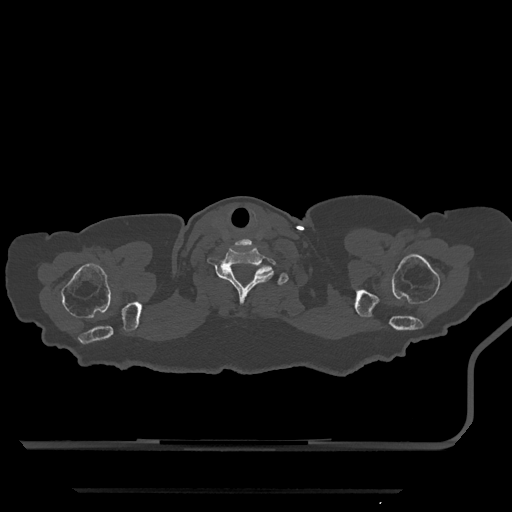
CT including the spine, one axial slice. Slice 735 of 797 in the series (ordered by position). Bone window (W 1800 / L 400 HU). 512 × 512 image matrix, field of view 440 × 440 mm. Female patient, age 51 years. Case-level facts recorded for this patient, not image findings: primary cancer: neuro; vertebrae with lytic lesions (as recorded): T8.
Annotated regions visible in this slice (semi-automatic segmentation, software-assisted and operator-edited):
- T1 vertebra: box from (x=264, y=269) to (x=289, y=286) px